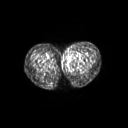
FDG PET of an extremity soft-tissue mass (from a PET/CT study), one axial slice. Position 41 of 267 along the scan axis. 3.27 mm slice thickness. 128 × 128 image matrix. Patient: female, 24 years. From the clinical record (not read from this slice): histological type: leiomyosarcoma; grade: high; site of the primary tumour: groin.
Annotated regions visible in this slice (expert contour drawn on MRI and transferred to this co-registered scan by the dataset authors):
- gross tumour volume including surrounding oedema: bounding box (x1, y1, x2, y2) in pixels: (61, 49, 79, 65)